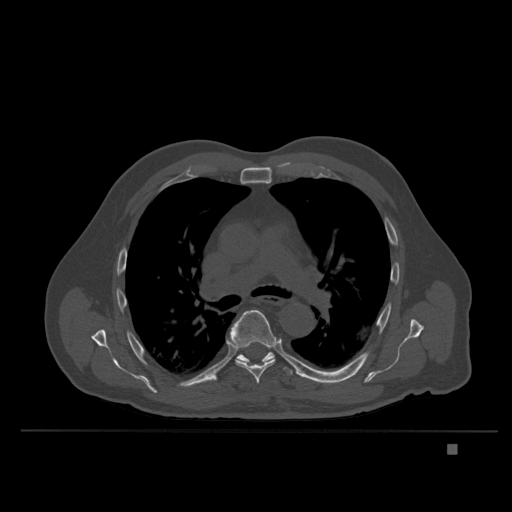
CT including the spine, one axial slice. Position 255 of 435 along the scan axis. Bone window (W 1800 / L 400 HU). 1.5 mm slice thickness. 512 × 512 image matrix. Male patient, age 73 years. From the clinical record (not read from this slice): primary cancer: skin.
Outlined on this slice (semi-automatic segmentation, software-assisted and operator-edited):
- T6 vertebra: bounding box (x1, y1, x2, y2) in pixels: (229, 310, 275, 384)
- T7 vertebra: (215, 351, 293, 381)